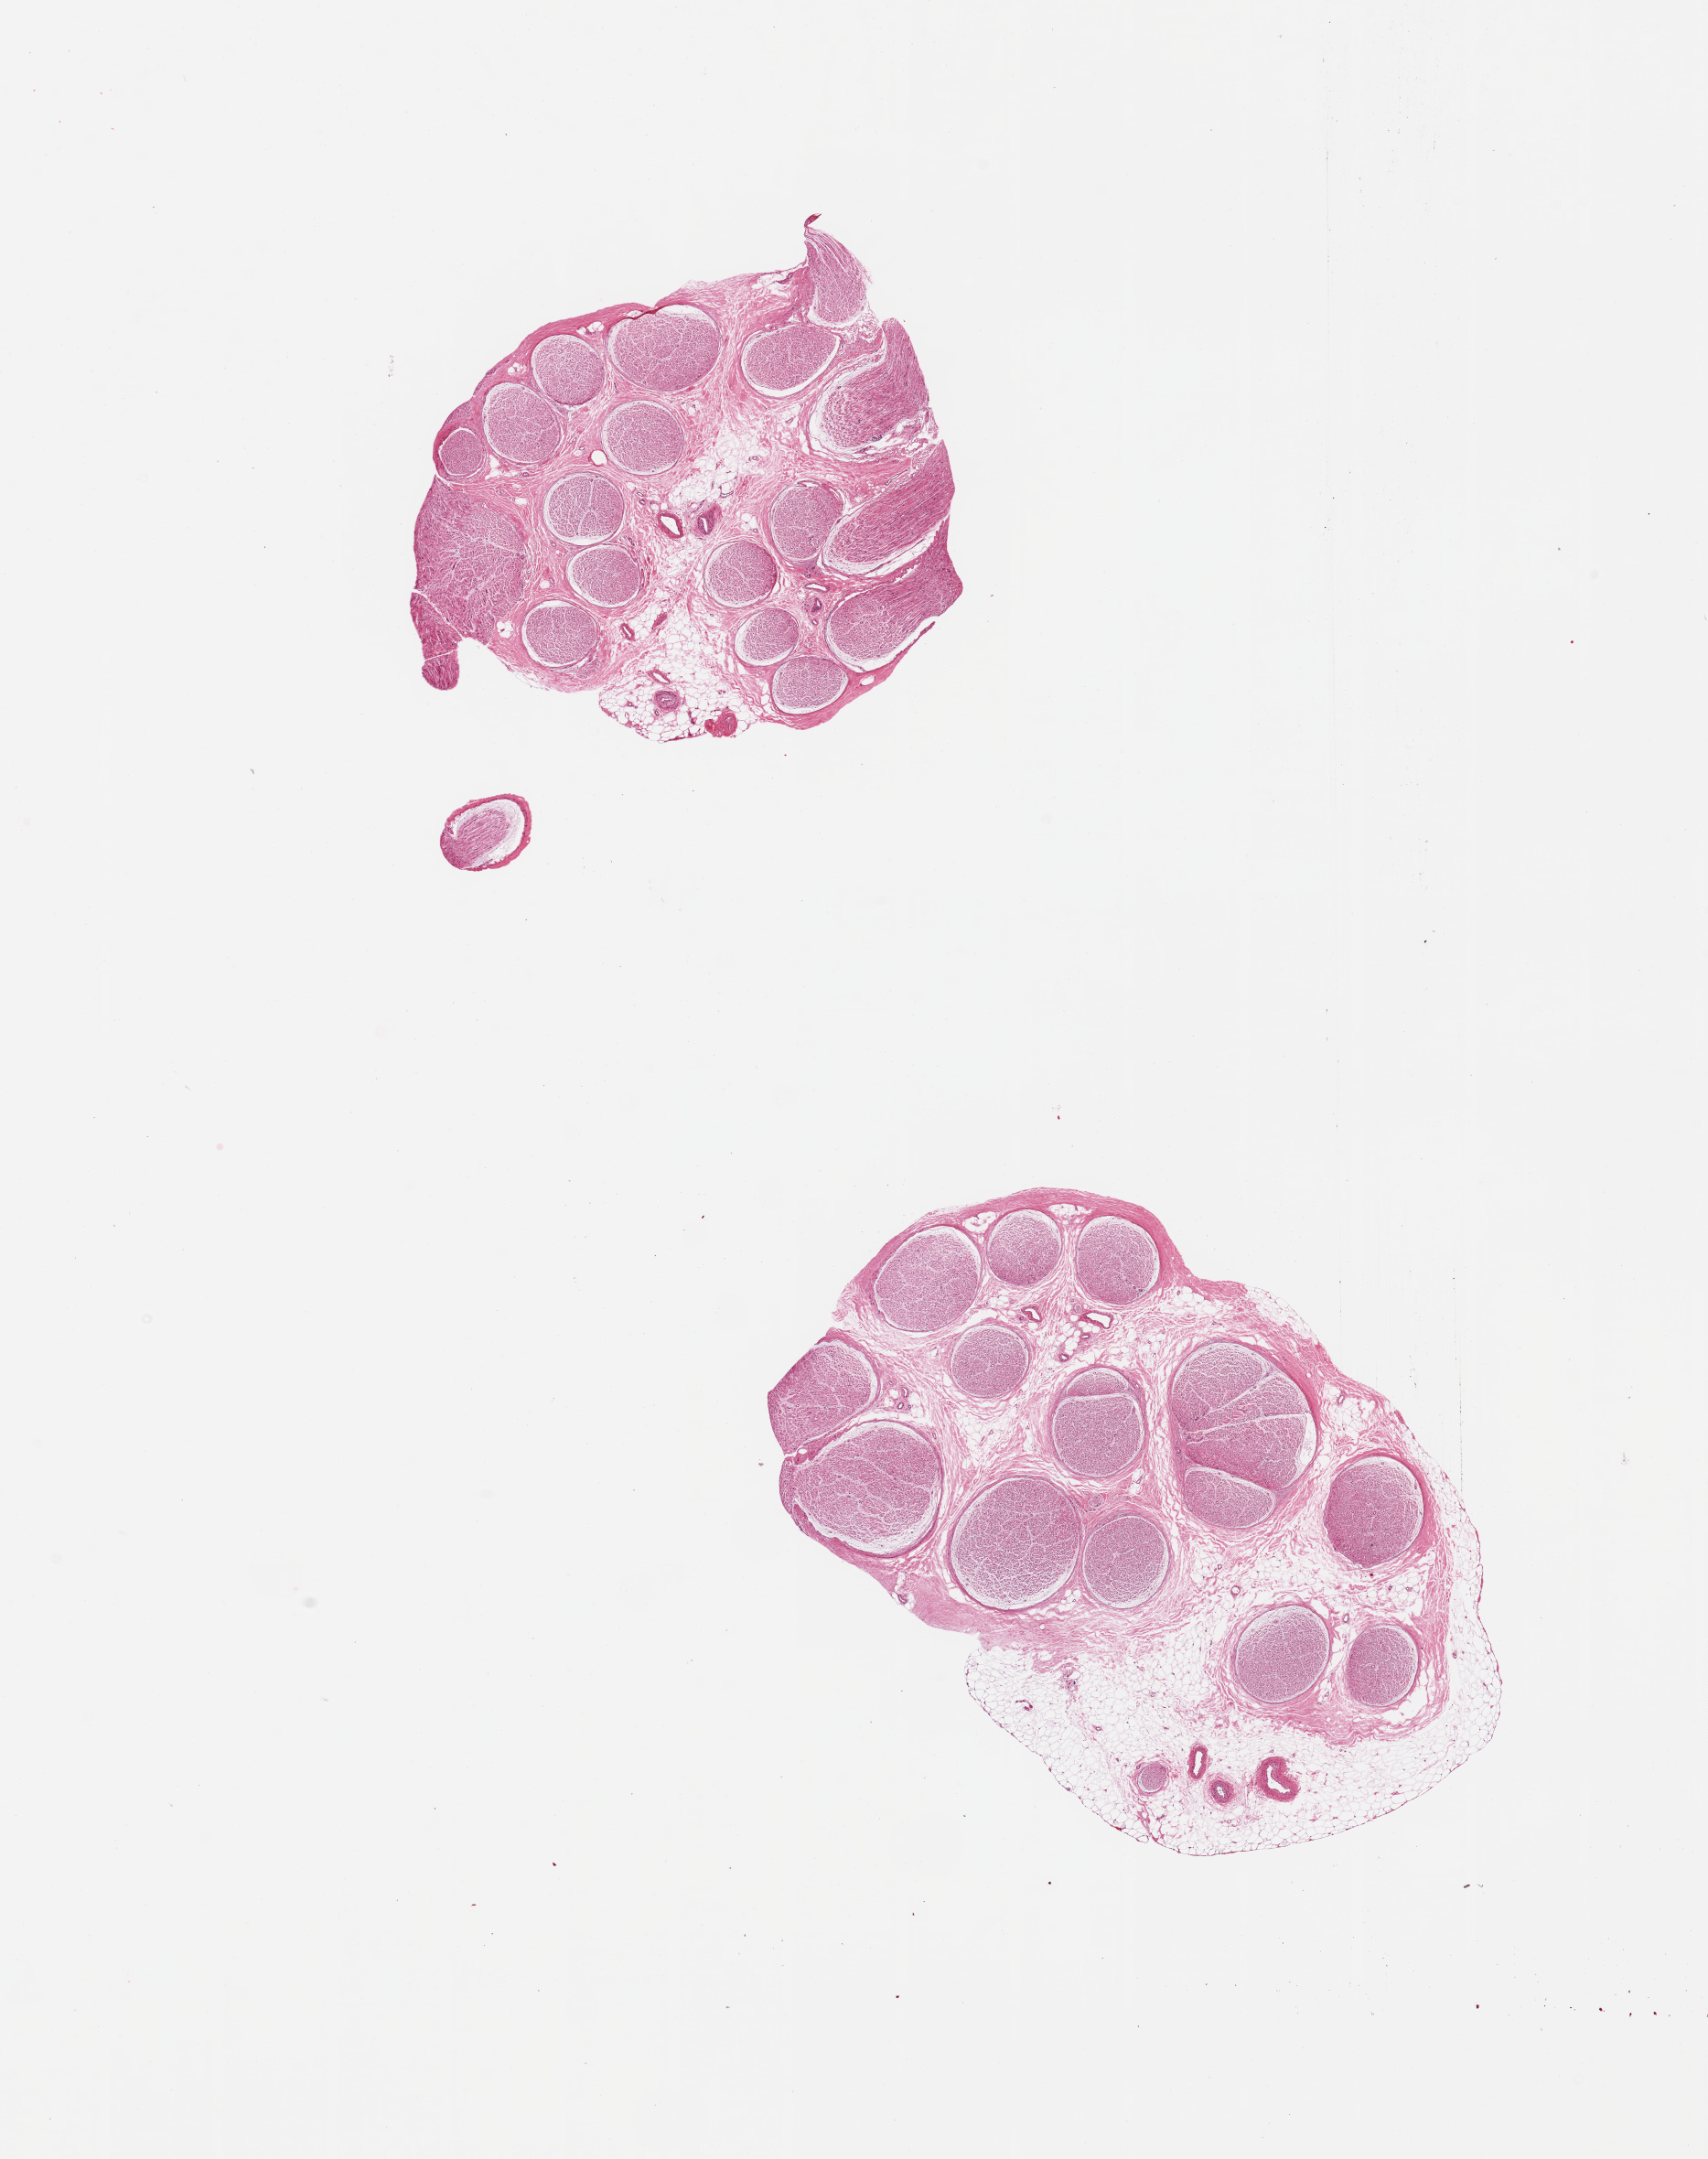
Whole-slide image, hematoxylin and eosin (H&E) stain, low-resolution overview of the scanned area, about 14.8 x 18.7 mm. PAXgene-fixed, paraffin-embedded tissue. Target tissue: tibial nerve. Tissue donor sample. Donor sex: female.
- reviewer comment on this tissue sample: 2 pieces; ~20% and 40% internal fat with fibrovascular component